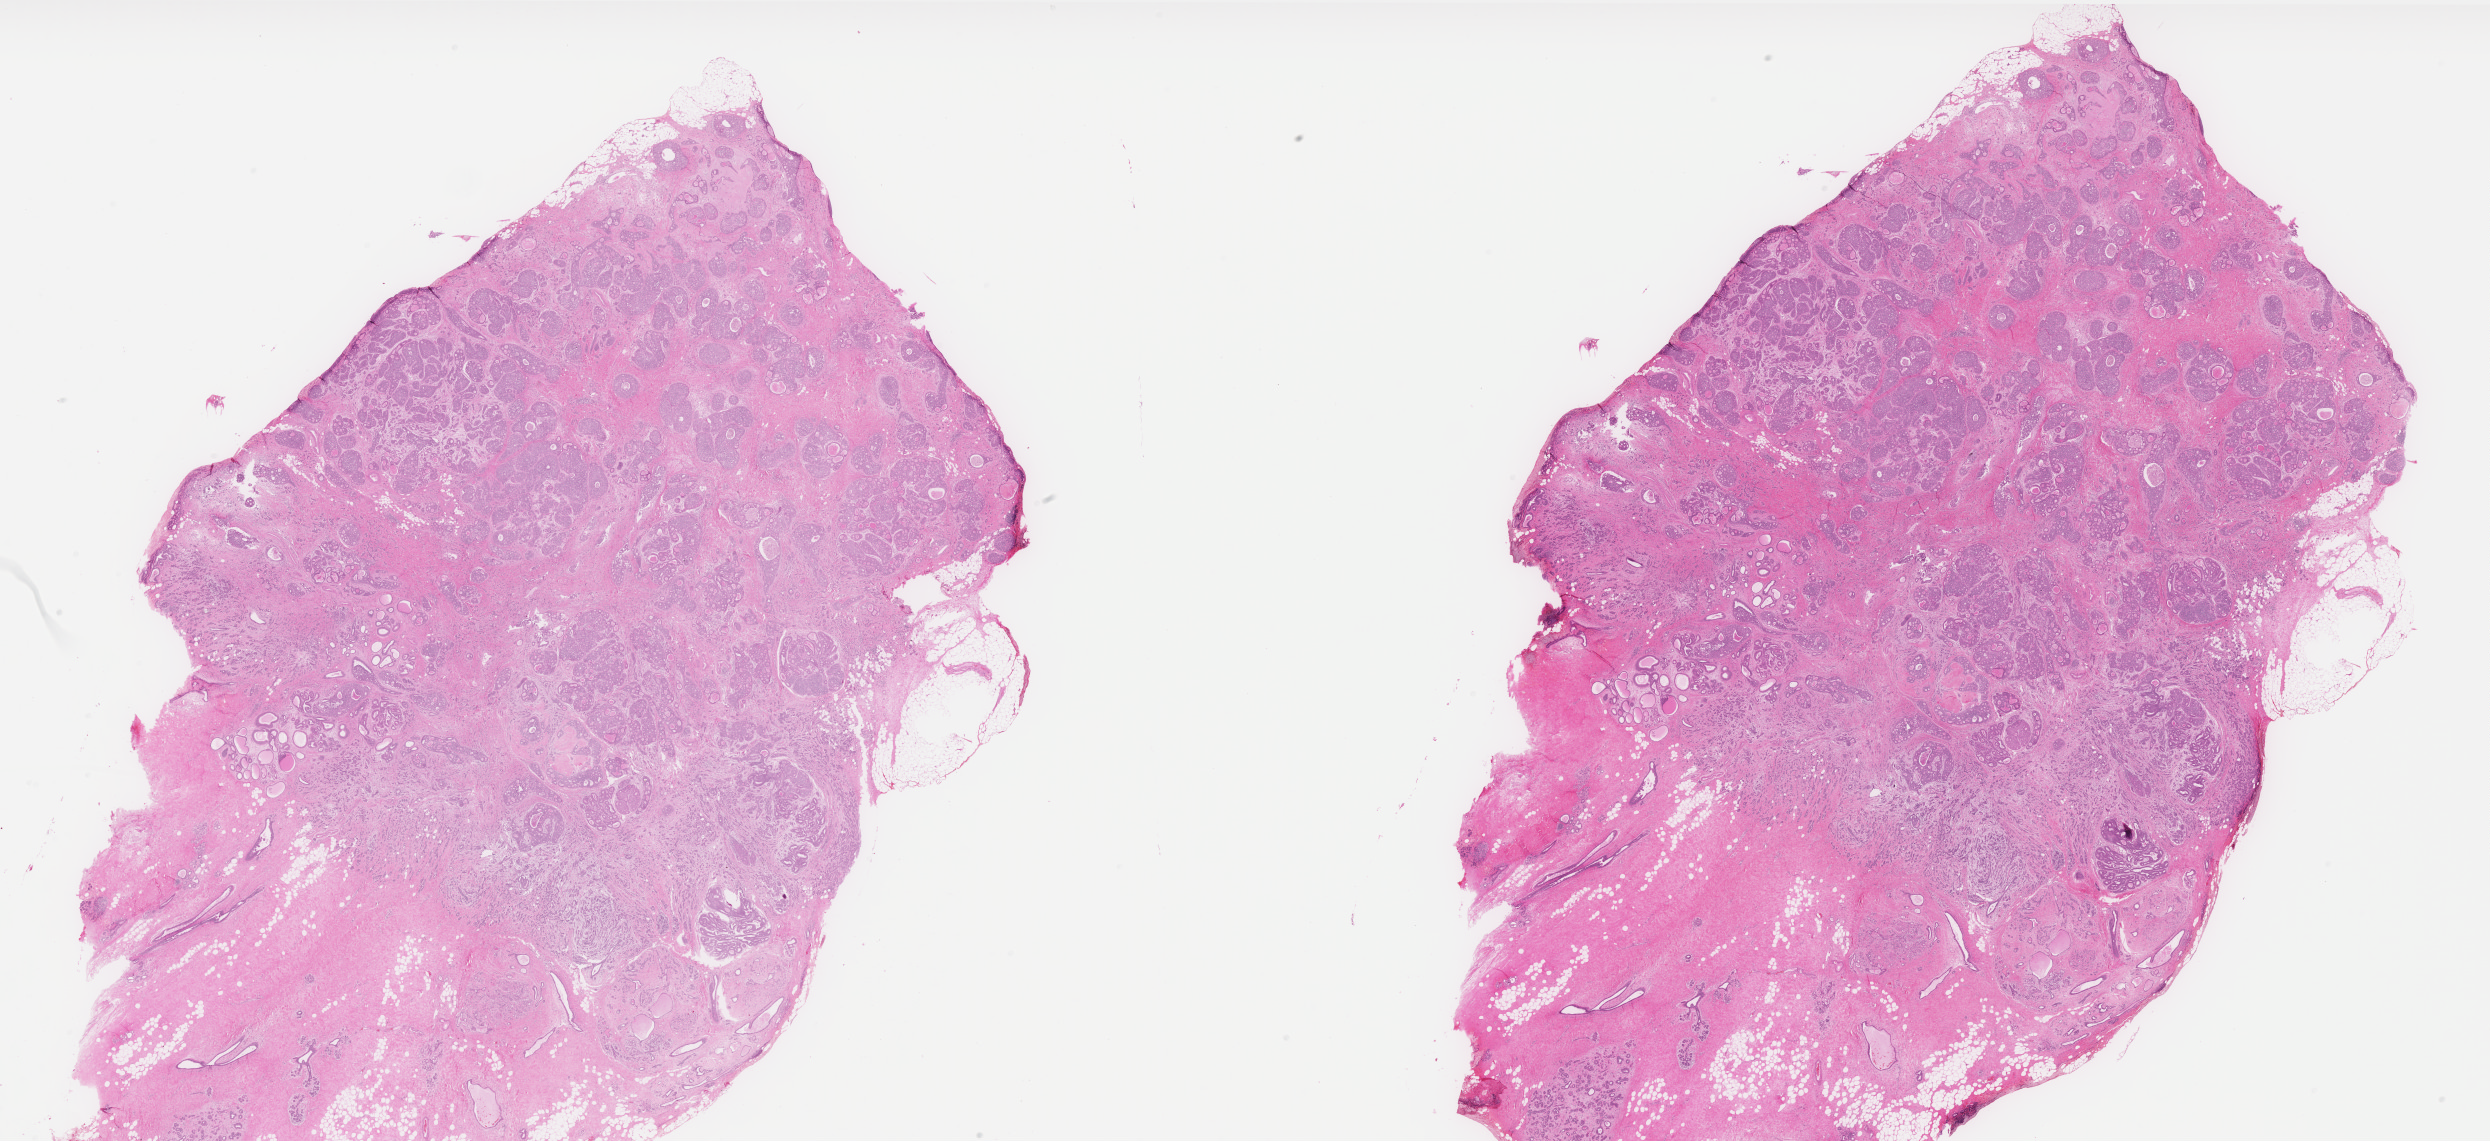
Whole-slide histology image, H&E — whole scanned area (about 39.9 x 18.3 mm, slide scanned at 40x) shown as a low-resolution overview. Formalin-fixed paraffin-embedded (FFPE) diagnostic section. Breast, primary tumour sample. Patient: female, age at initial diagnosis 41 years.
AJCC pathologic stage: IIB (6th edition). Histologic diagnosis: Infiltrating duct carcinoma, NOS.